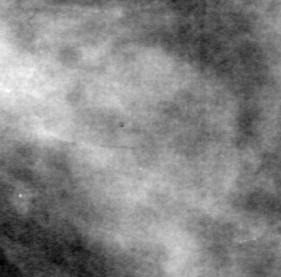
Crop from a digitized film mammogram around one marked abnormality; left breast; CC view; BI-RADS breast density category 4 (scale 1–4).
Finding: mass, shape round, margins circumscribed; BI-RADS assessment category 4; subtlety rating 3 on a 1 (subtle) to 5 (obvious) scale; pathology (as recorded): benign.